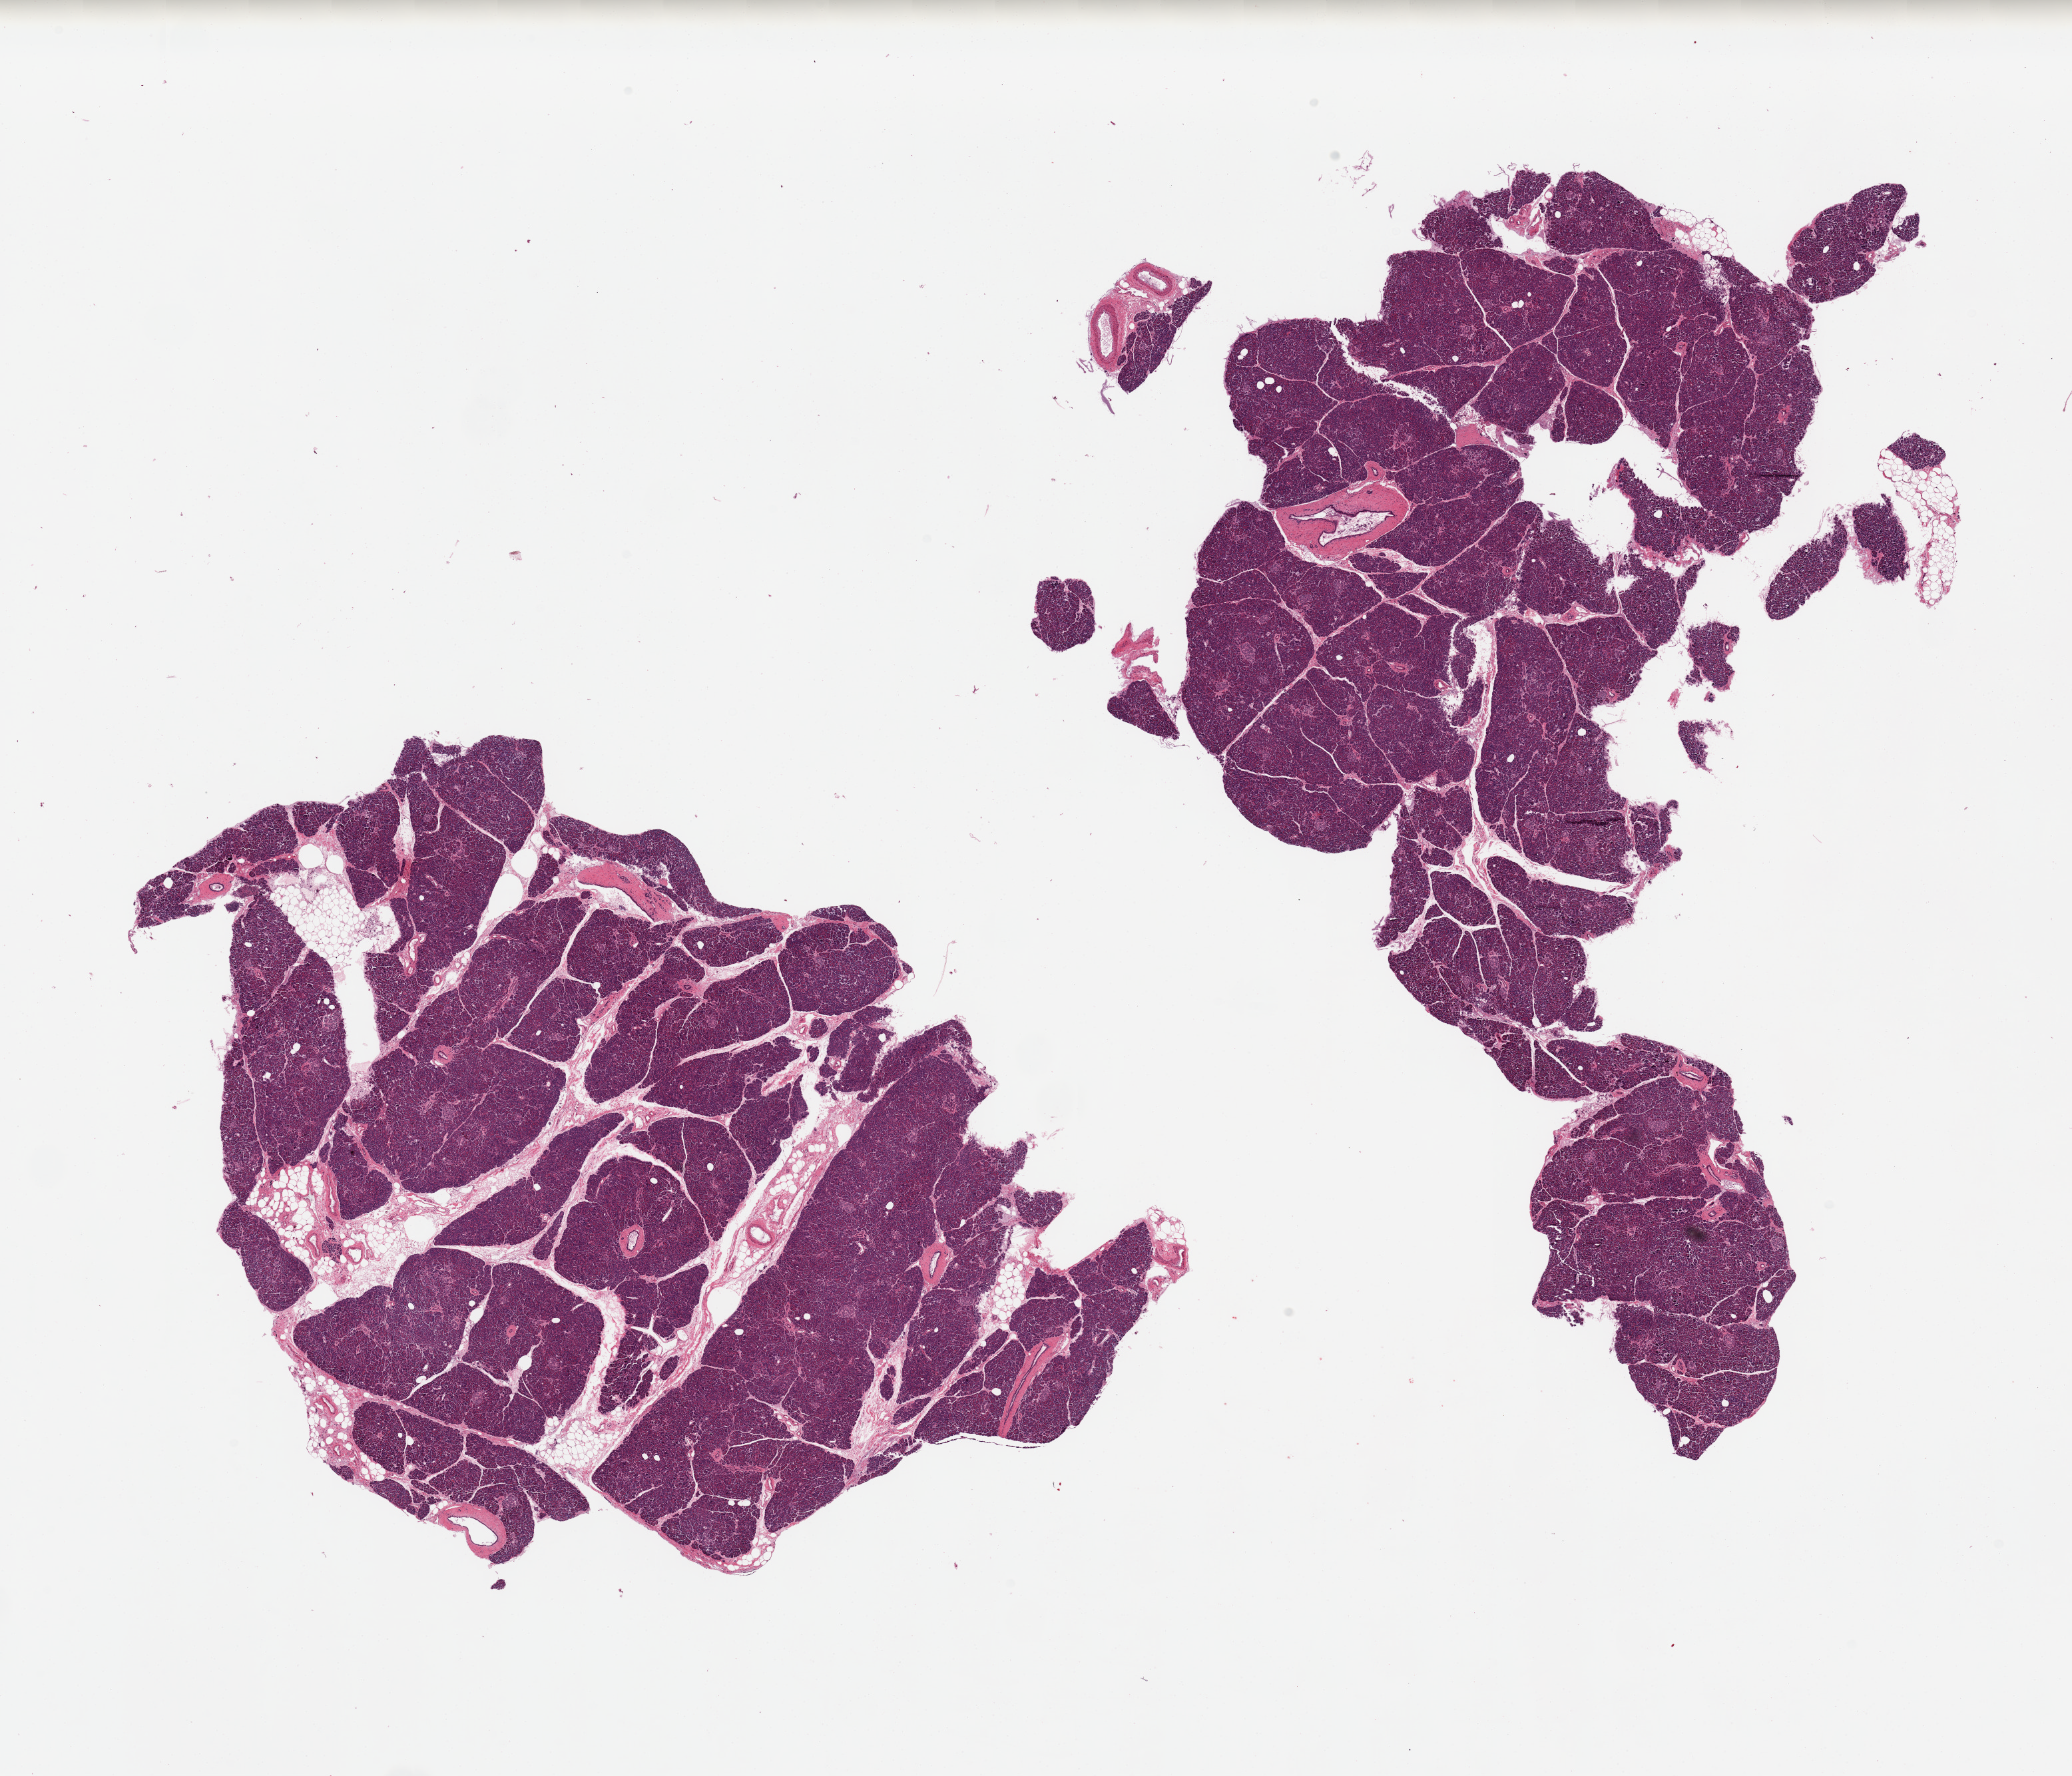
Whole-slide image, haematoxylin and eosin stain, low-resolution overview of the scanned area, about 24.6 x 21.1 mm (from a 20x scan), PAXgene-fixed, paraffin-embedded tissue, sampled site (target tissue): pancreas, donor tissue sample.
Pathologist's review note for this sample: 2 pieces; well trimmed.